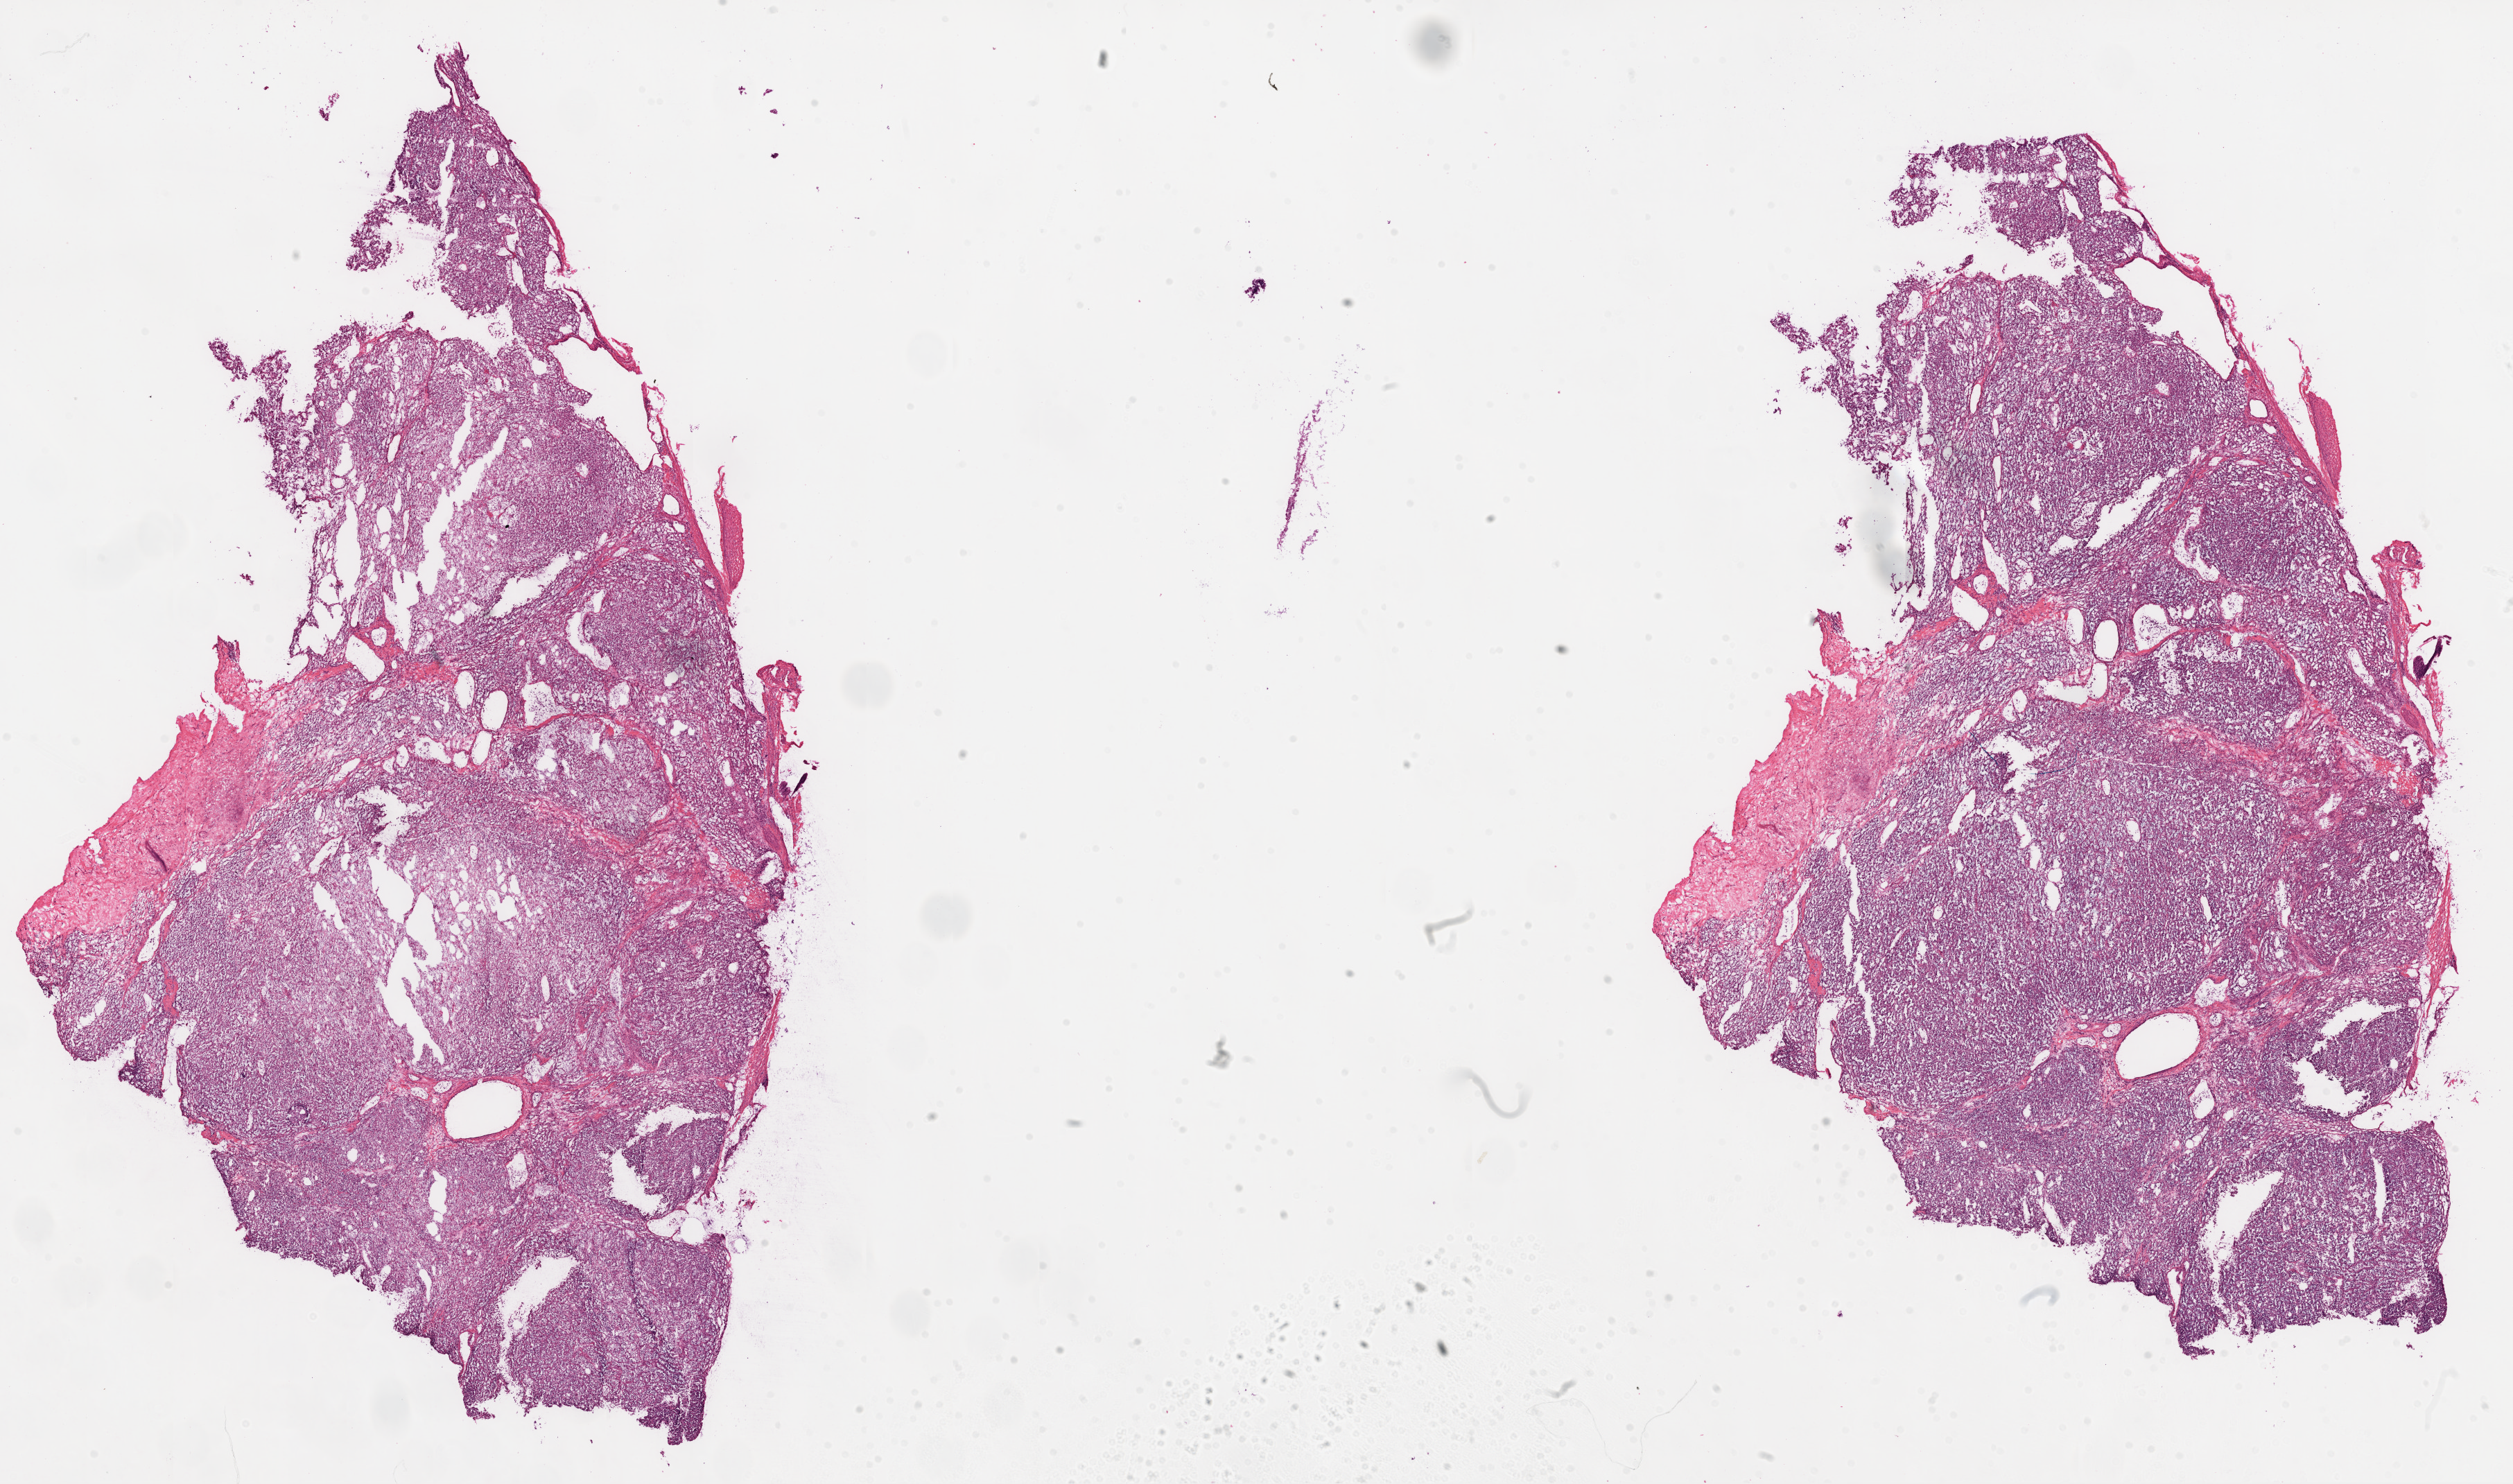
Hematoxylin and eosin (H&E) stained whole-slide image, shown as a low-resolution overview of the whole scanned area (about 29.1 x 17.2 mm), frozen section from the top of the tissue portion, kidney, primary tumour sample. Male, age 59 years at initial diagnosis. Histologic grade: G2 (moderately differentiated). Pathologist review of this section (percent, as recorded): tumour cells 85%, tumour nuclei 85%, normal cells 0%, stromal cells 15%, necrosis 0%.
* laterality: right
* histologic diagnosis: Clear cell adenocarcinoma, NOS
* AJCC pathologic stage: I